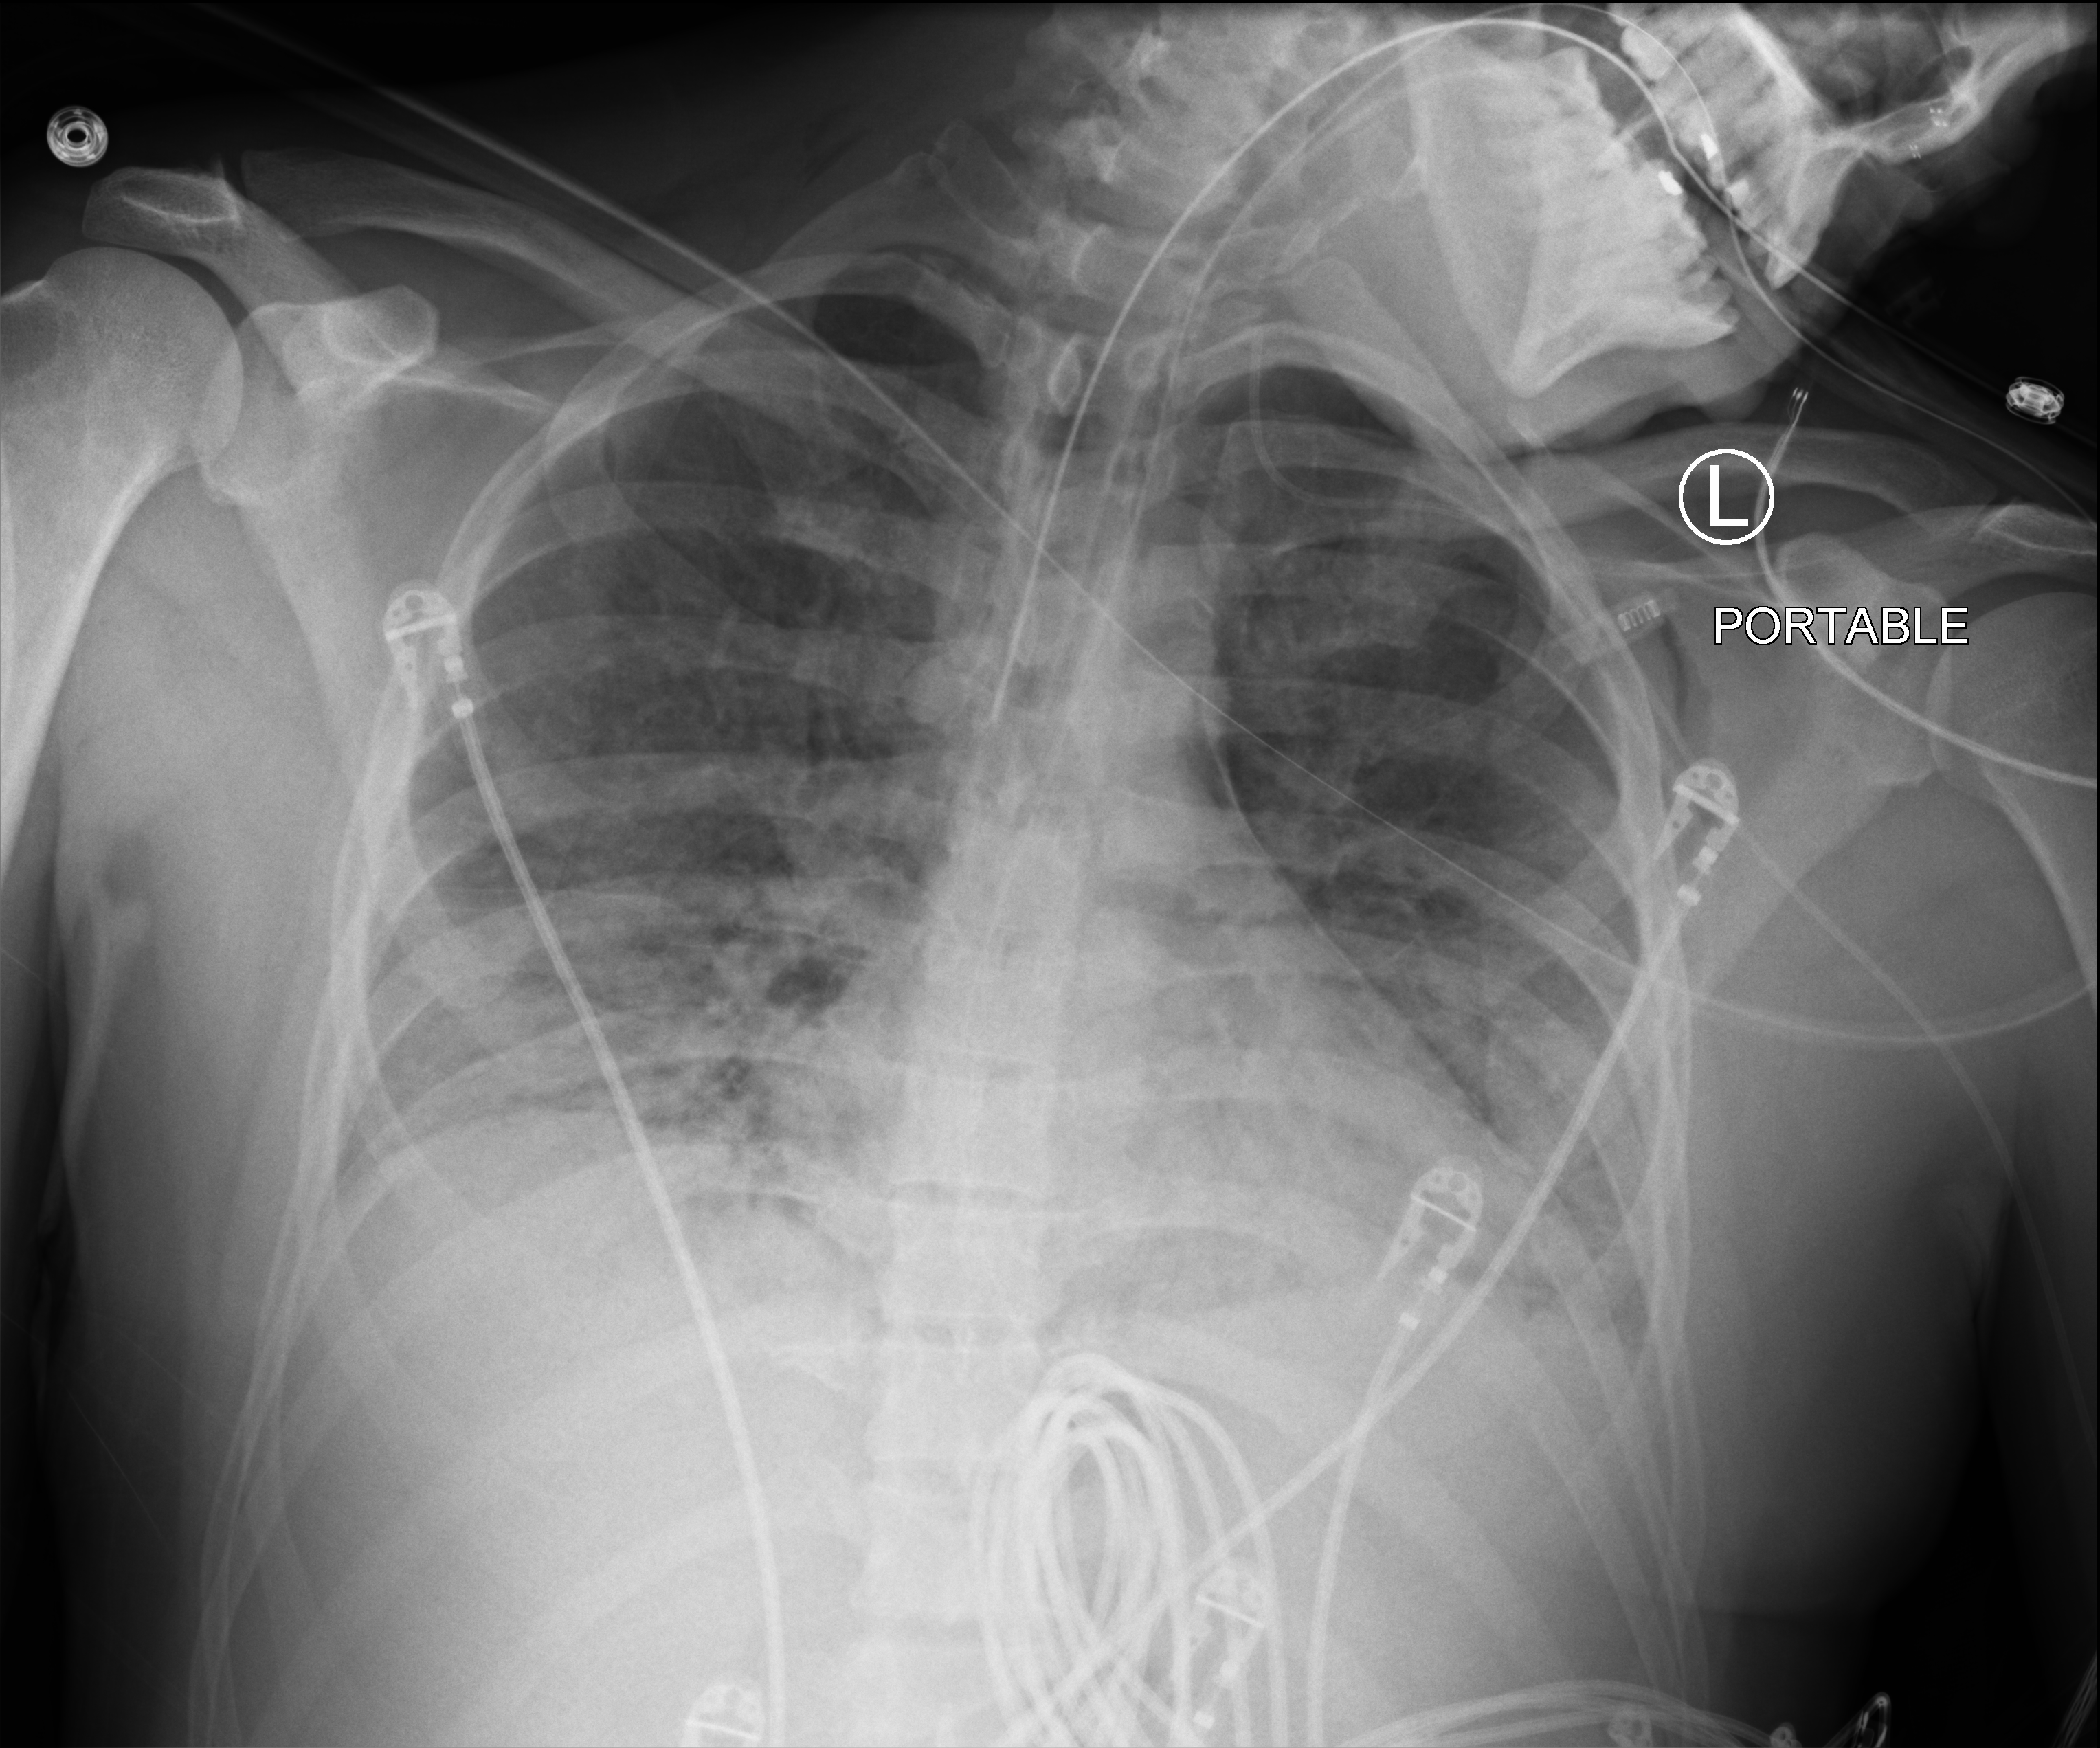
Chest X-ray (portable), anteroposterior (AP) projection. Patient hospitalised with COVID-19; male, aged 18–59 years.
Admission-level facts for this patient (not findings on this image; timing relative to this image not recorded): diabetes (admission record): no; mechanically ventilated during this hospital stay: yes.